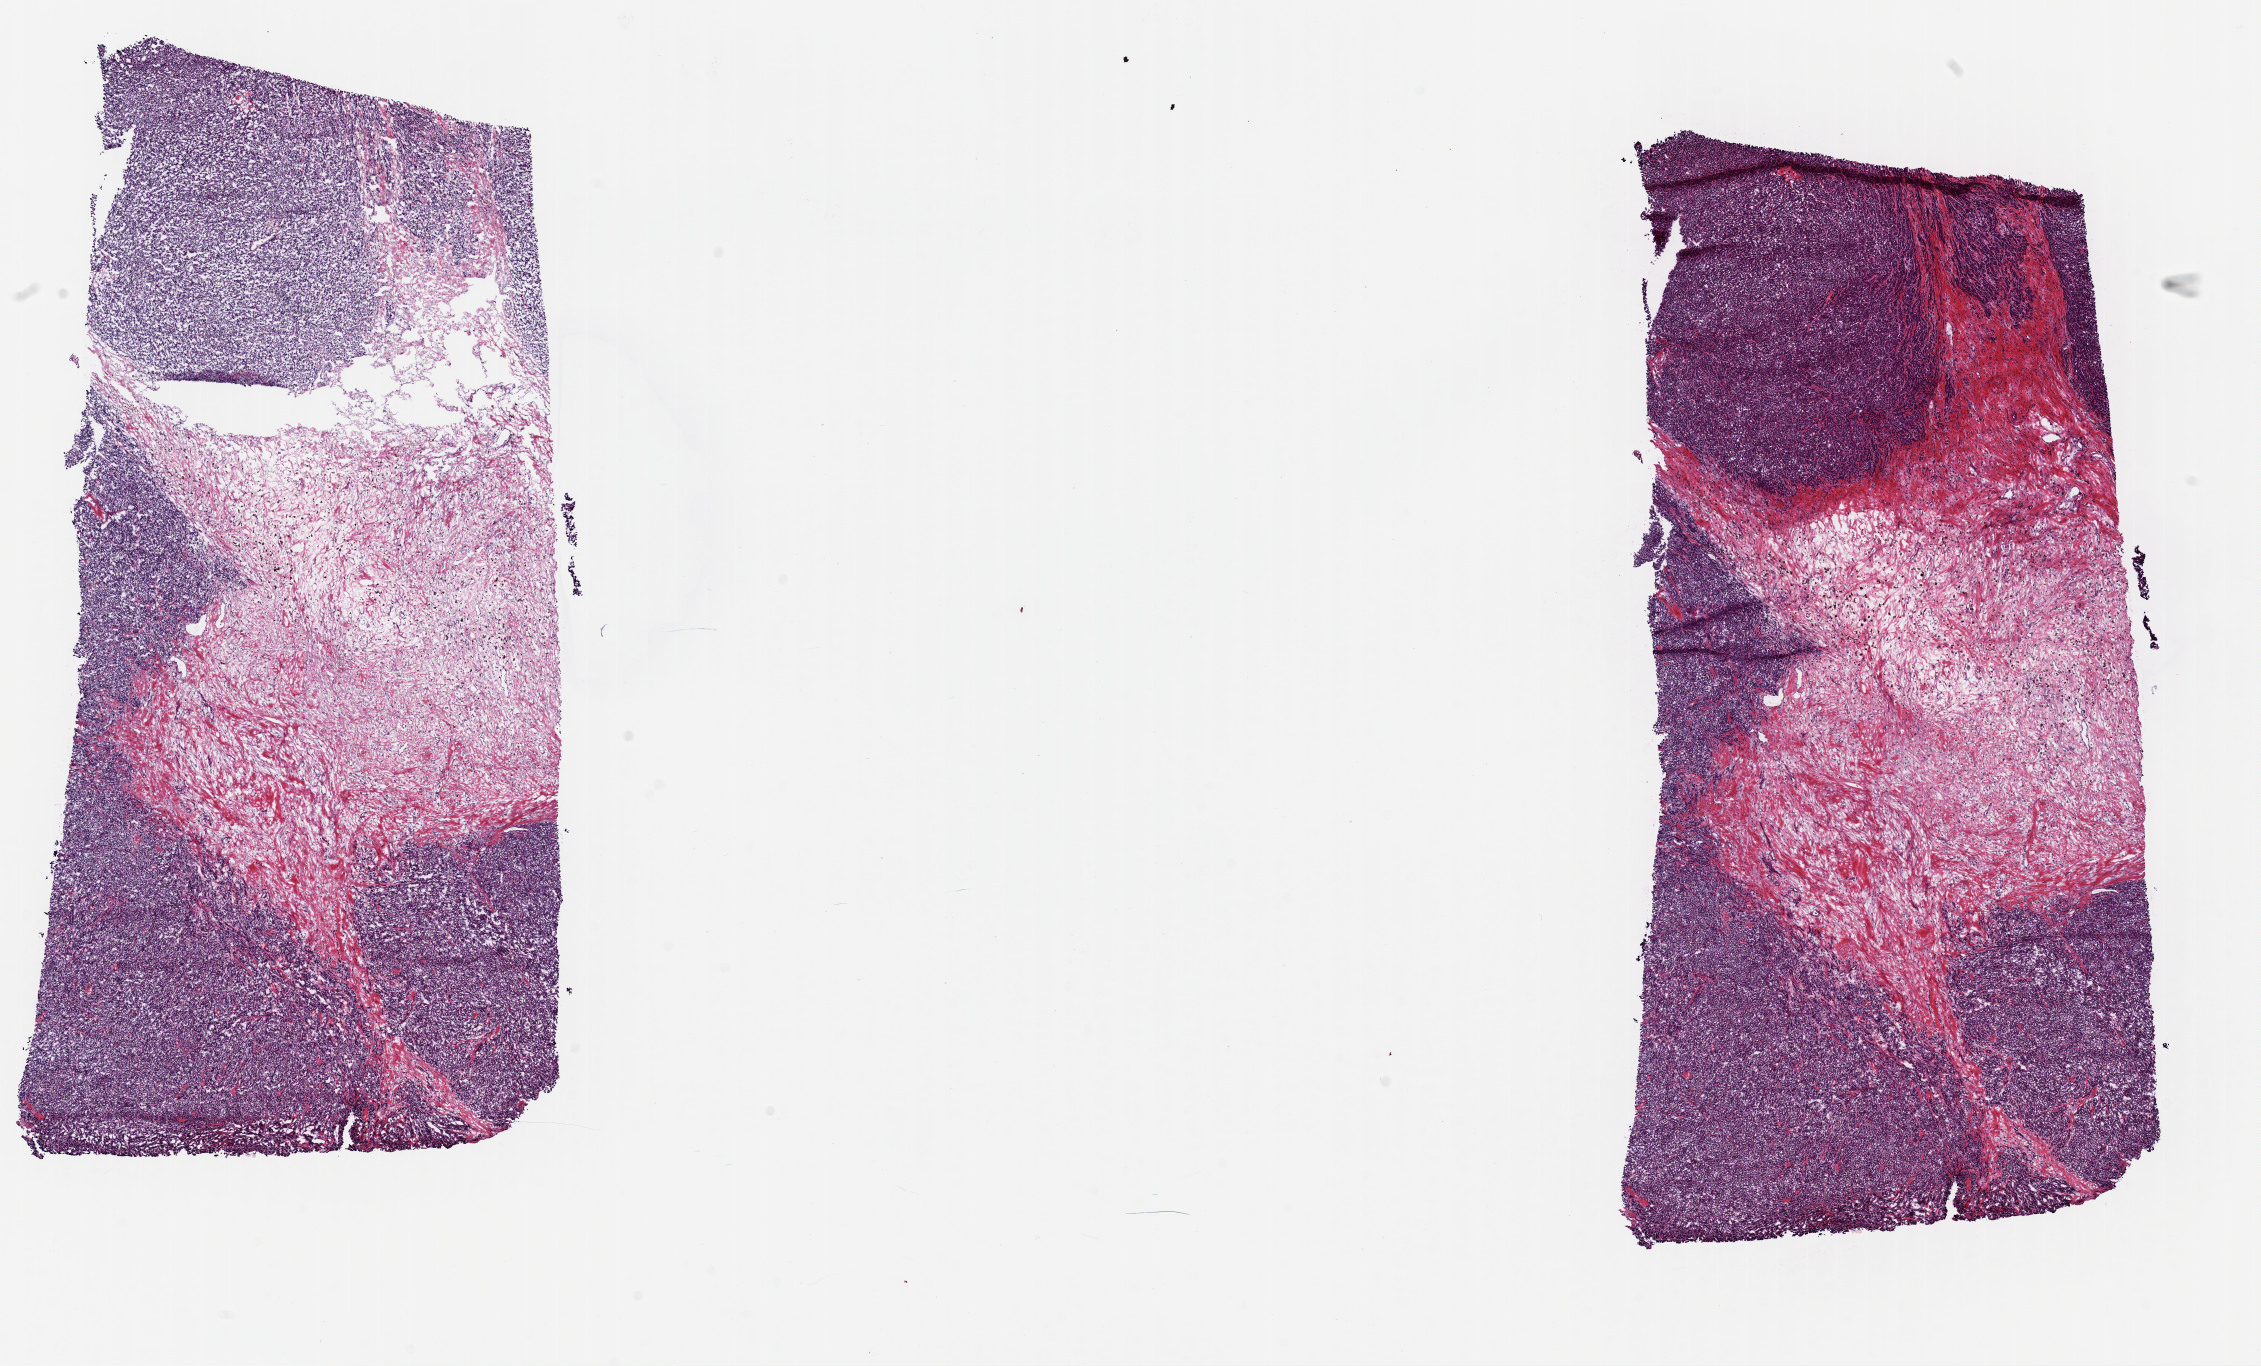
Digitized Hematoxylin and eosin (H&E) stained tissue section (whole slide), shown as a low-resolution overview of the whole scanned area (about 17.9 x 10.8 mm). Frozen section. Metastatic tumour sample. Male, age 60 years at initial diagnosis.
This section: metastatic tumour tissue. Patient diagnosis: Malignant melanoma, NOS.